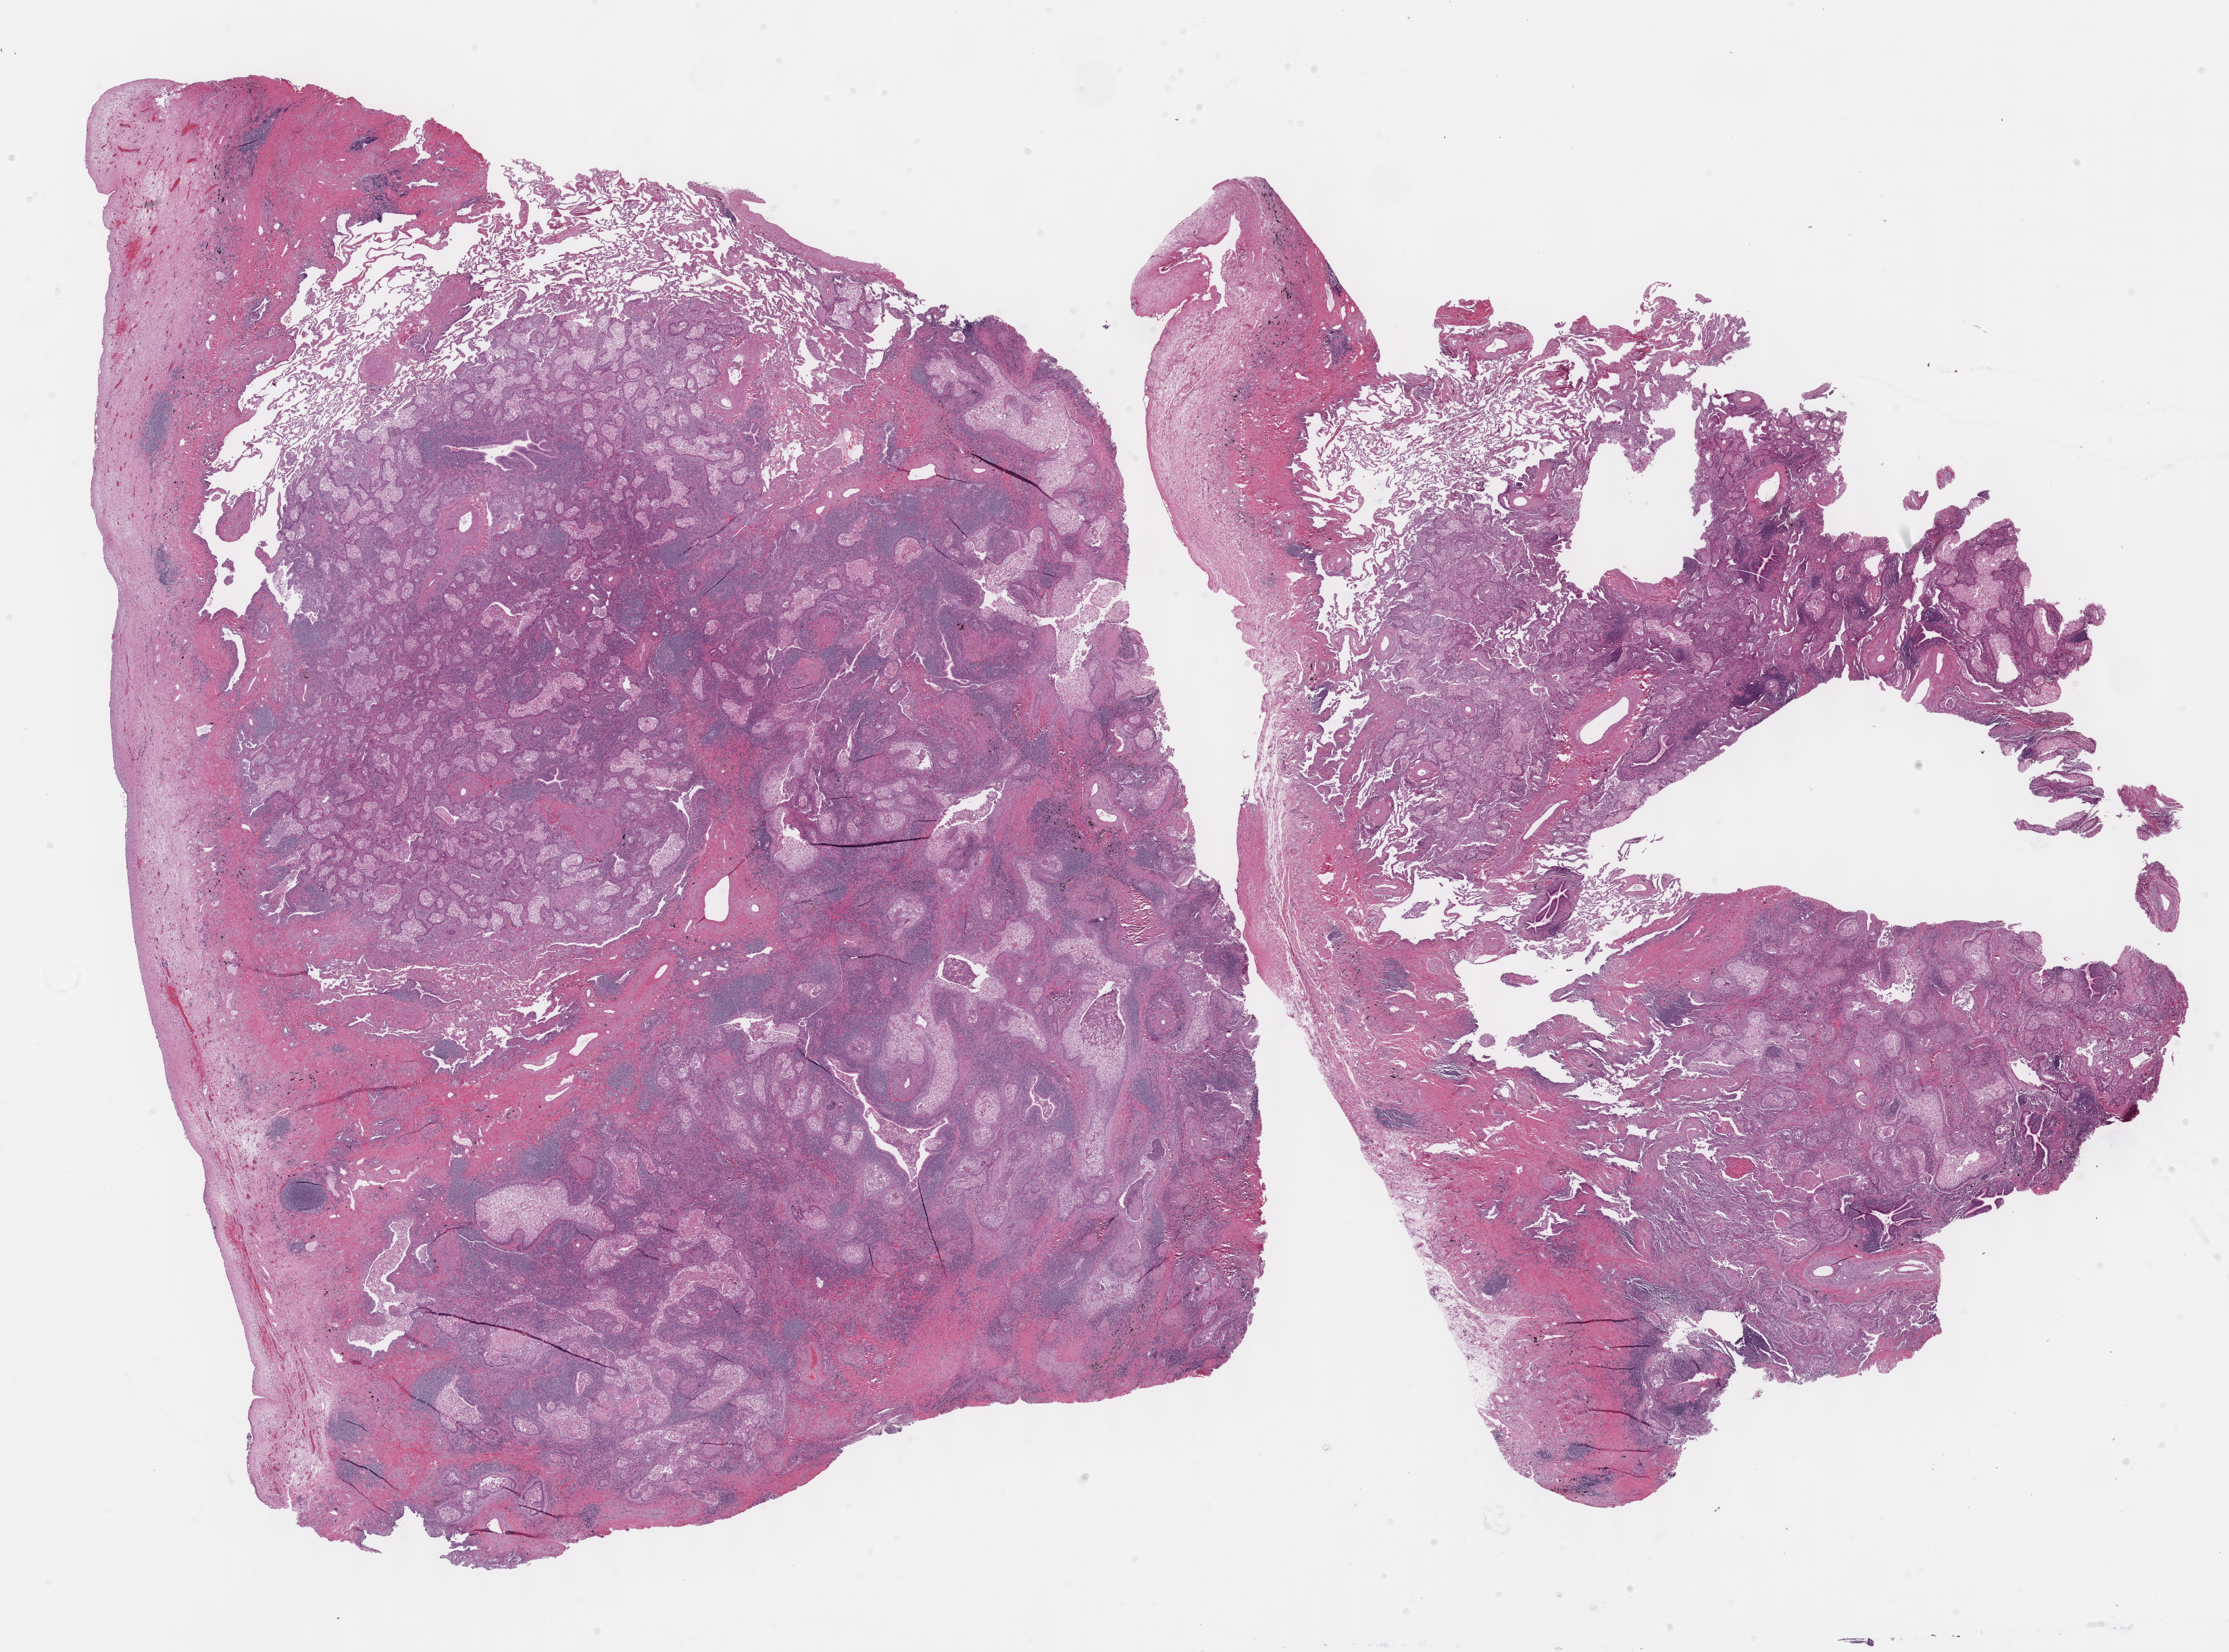
Digitized H&E tissue section (whole slide), shown as a low-resolution overview of the whole scanned area (about 26.7 x 19.8 mm, acquisition: 40x scan), FFPE section, sample: primary tumour, lung. Female patient; age at initial diagnosis 80 years.
- pathologic diagnosis: Squamous cell carcinoma, NOS
- AJCC pathologic stage: IB